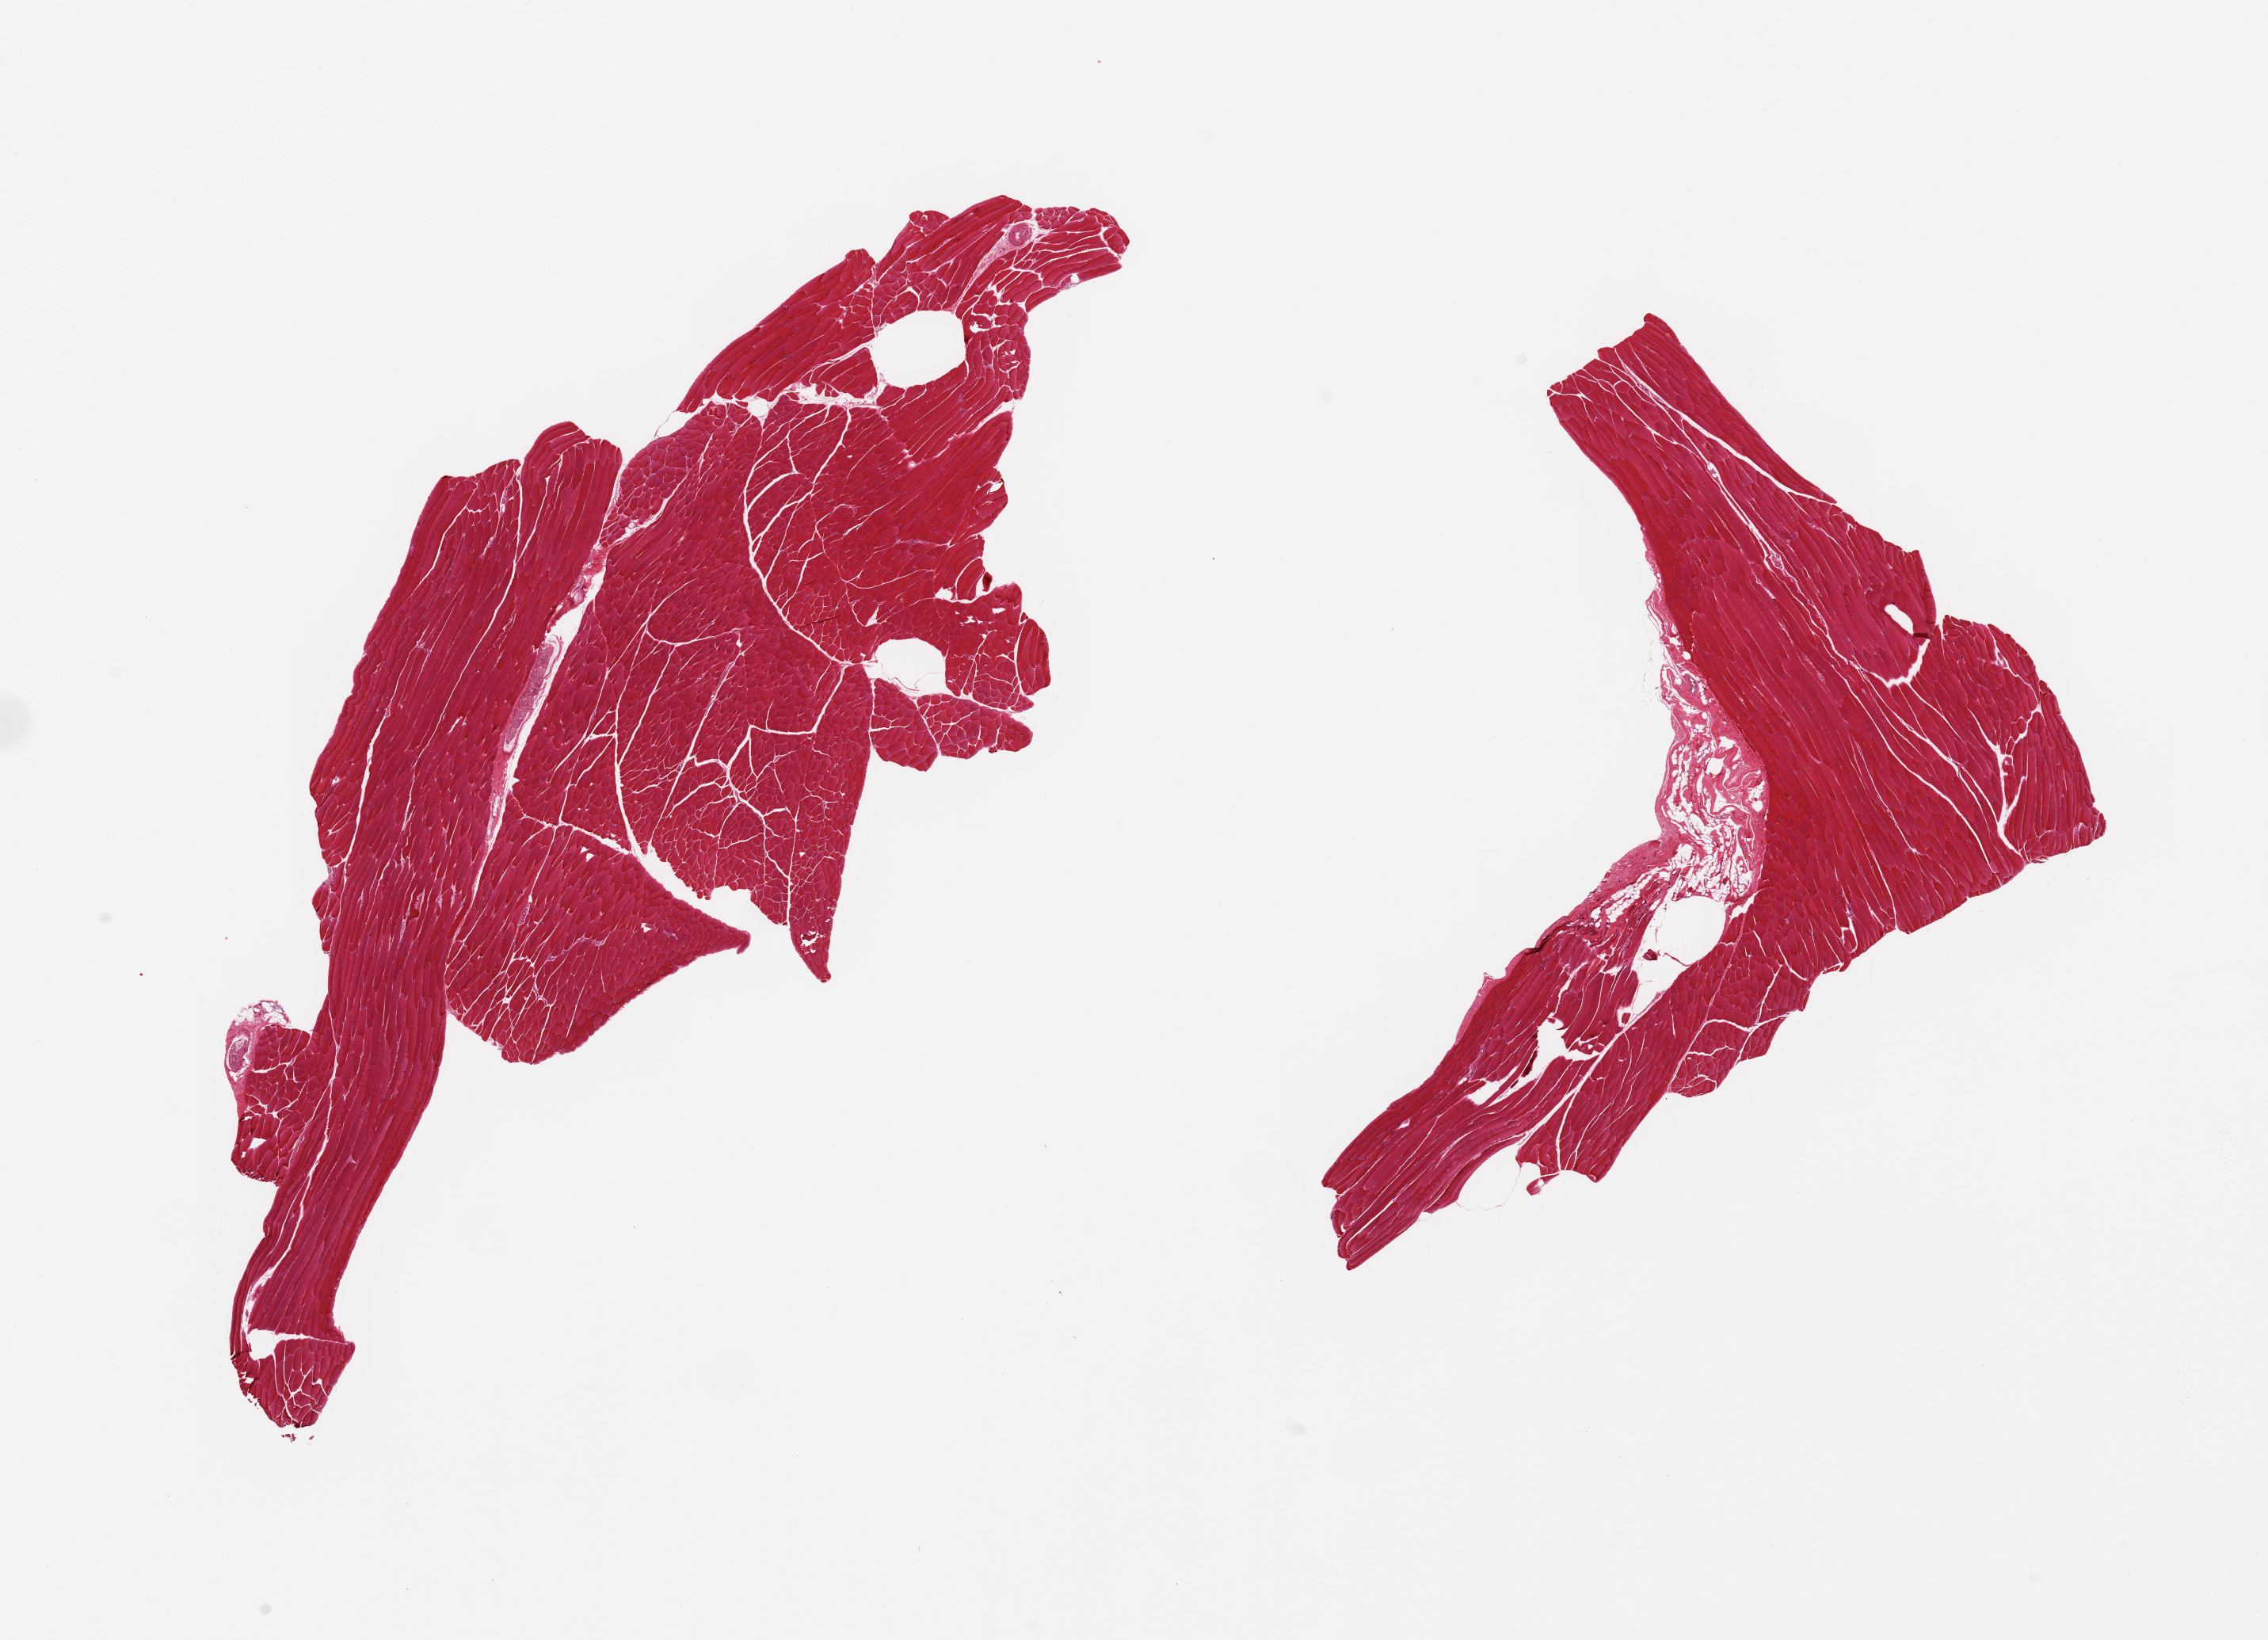
Digitized hematoxylin and eosin (H&E)-stained section, brightfield, low-resolution overview of the scanned area, about 22.6 x 16.4 mm (from a 20x scan), PAXgene-fixed paraffin-embedded (PFPE) section, sampled site (target tissue): skeletal muscle, tissue donor sample. Donor sex: male.
Review note (as recorded): 2 pieces, ~10% adherent/interstitial fat.